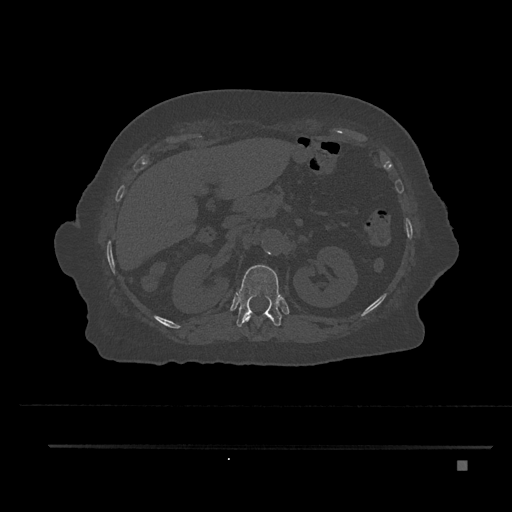
CT including the spine, one axial slice. Position 273 of 797 along the scan axis. Reconstruction kernel Br40s/3. Bone window (W 1800 / L 400 HU). 0.5 mm slice thickness. 512 × 512 image matrix. Patient: female, 76 years. From the clinical record (not read from this slice): primary cancer: lung; vertebrae with lytic lesions (as recorded): T11, L3.
Annotated regions visible in this slice (semi-automatically segmented with operator editing):
- T11 vertebra: bounding box (x1, y1, x2, y2) in pixels: (243, 313, 262, 340)
- T12 vertebra: (236, 265, 283, 327)